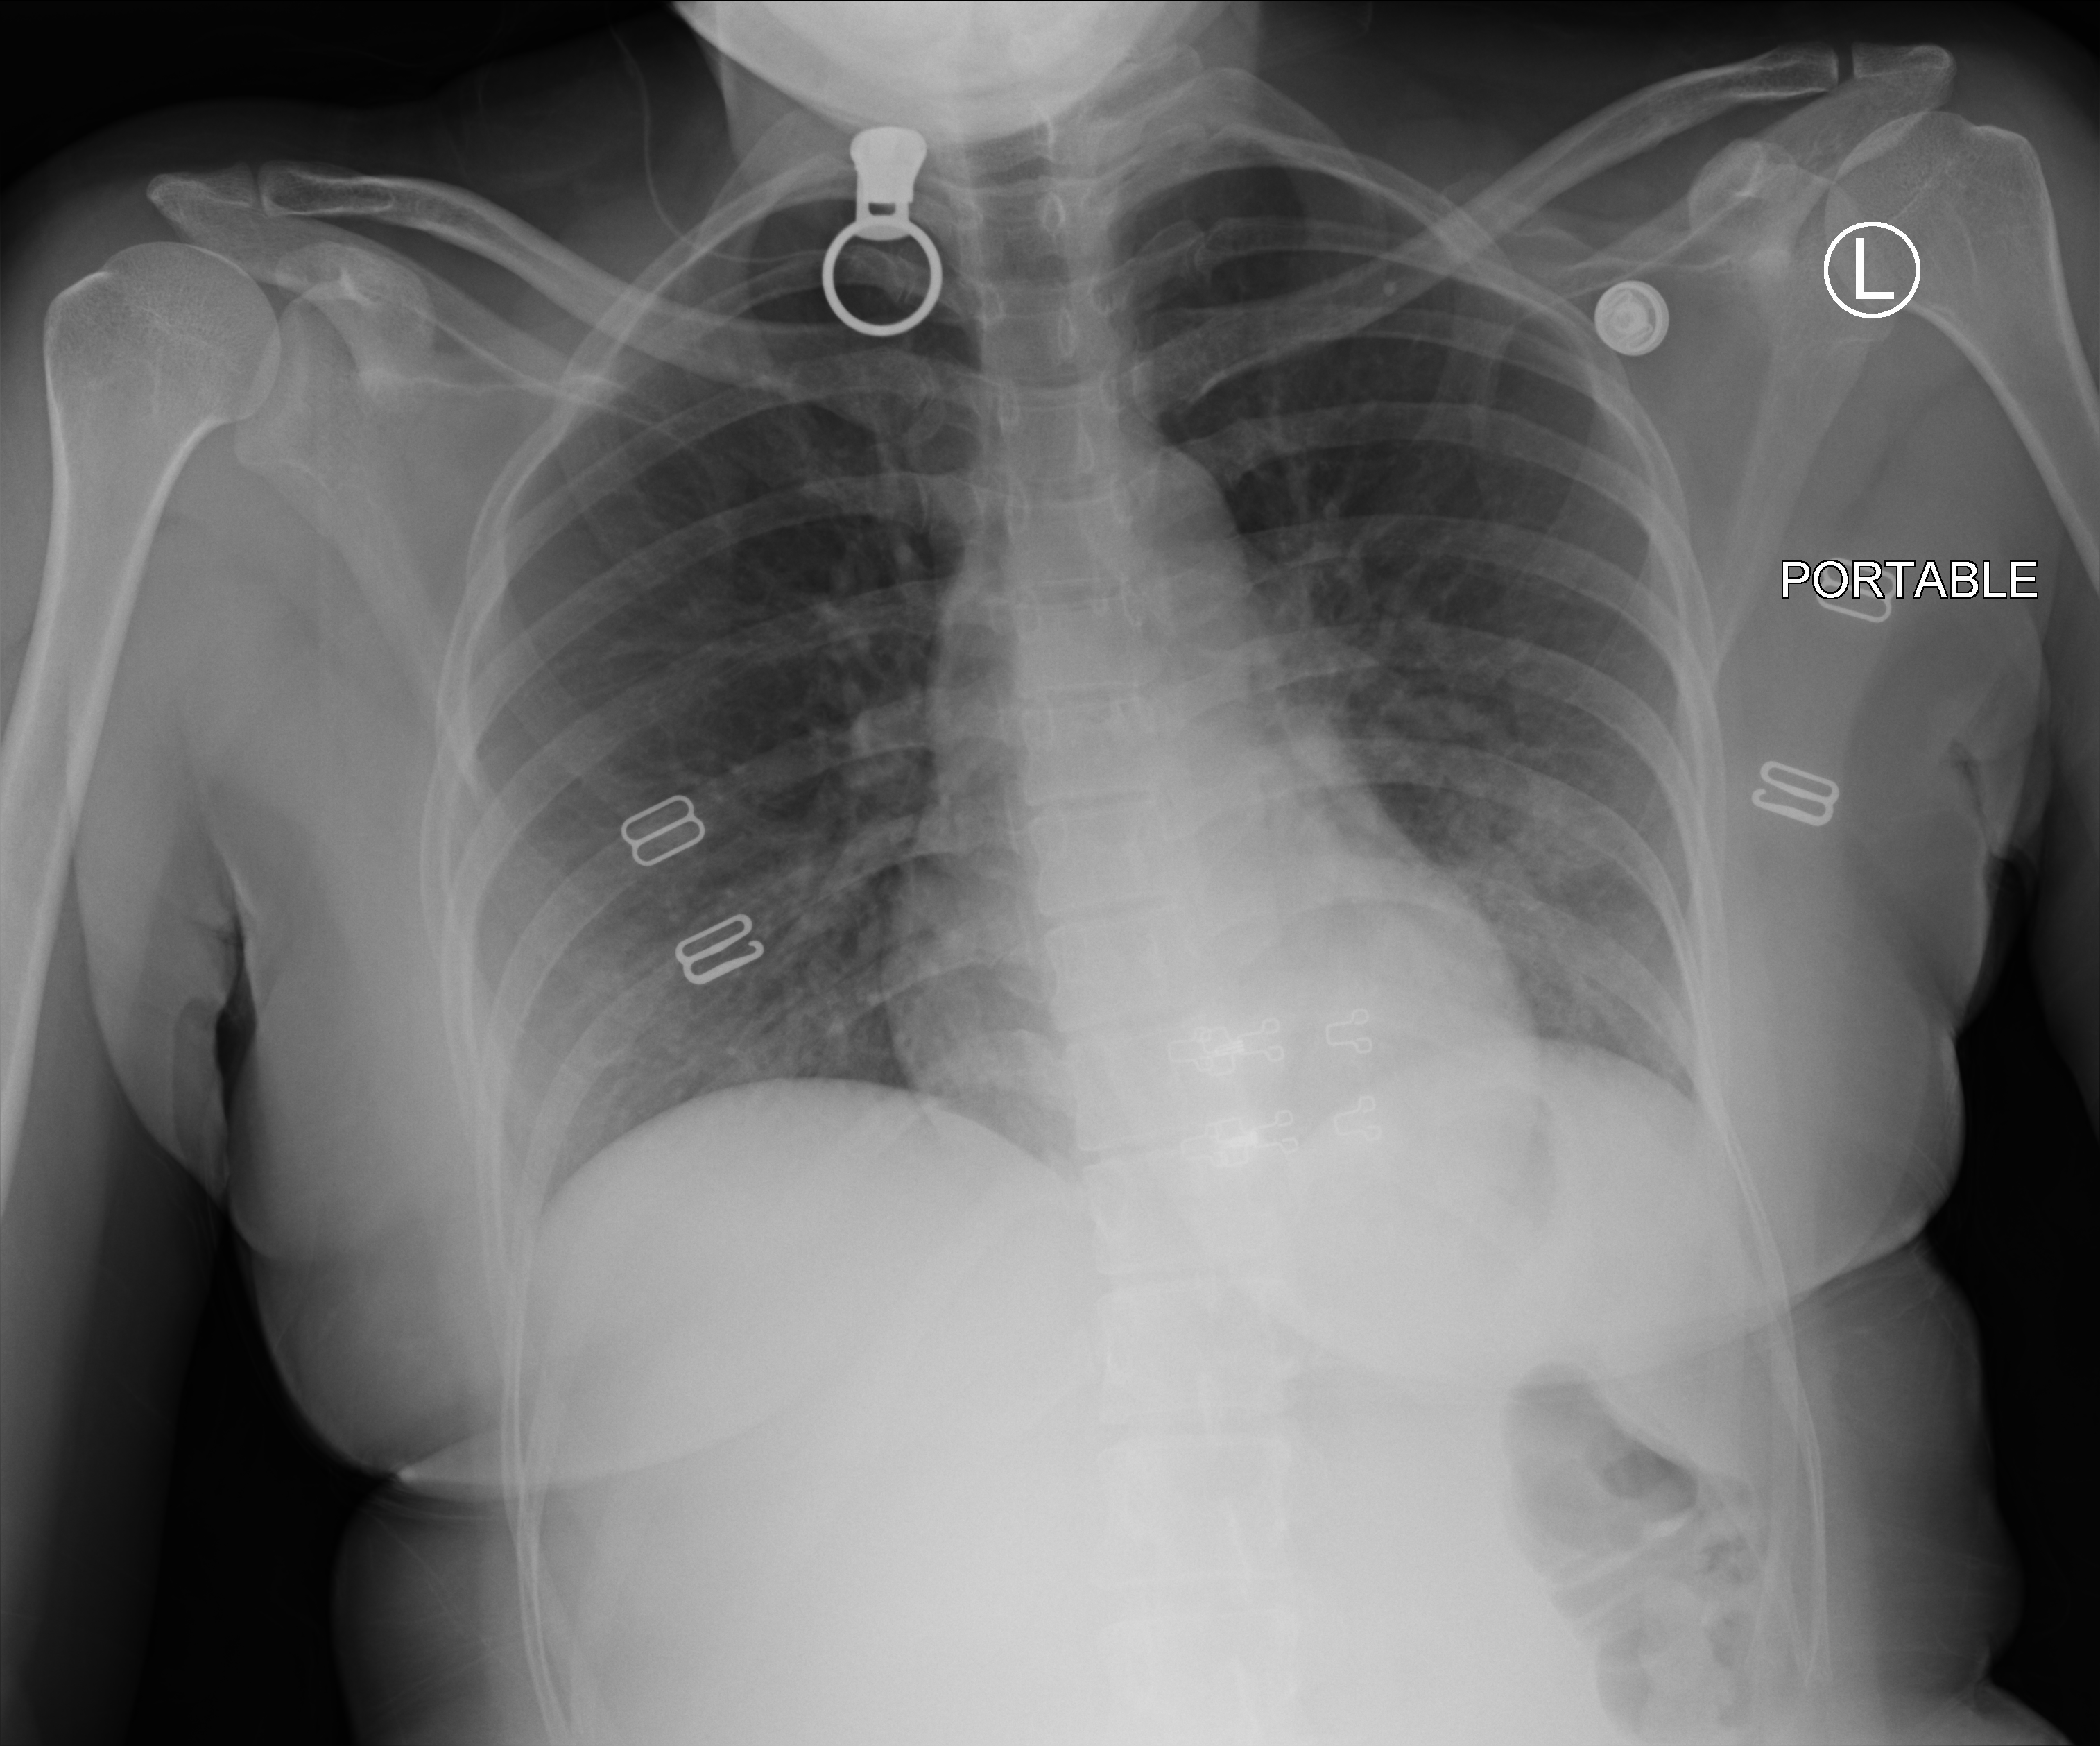
Bedside chest radiograph (computed radiography); anteroposterior (AP) projection. Patient hospitalised with COVID-19; female, aged 18–59 years.
From the hospital-stay record, not from the radiograph (when in the stay this image was taken is not recorded):
- other chronic lung disease (admission record): no